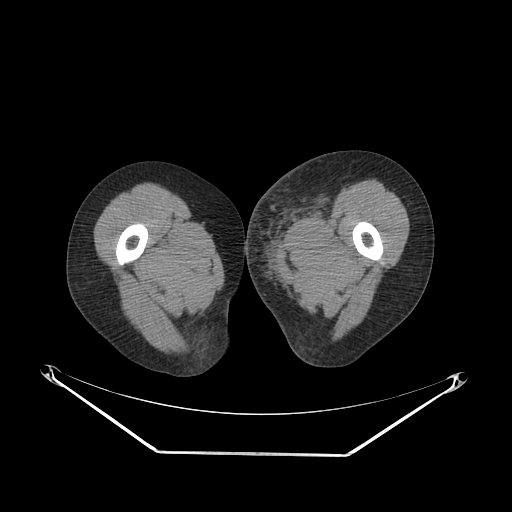
CT of an extremity soft-tissue mass (from a PET/CT study), one axial slice. Position 43 of 267 along the scan axis. 140 kVp. Soft-tissue window (W 400 / L 40 HU). 3.75 mm slice thickness. 512 × 512 image matrix, field of view 500 × 500 mm. Female patient. From the clinical record (not read from this slice): histological type: leiomyosarcoma; grade: high; site of the primary tumour: groin.
Structures marked on this image (expert contour drawn on MRI and transferred to this co-registered scan by the dataset authors):
- gross tumour volume including surrounding oedema: bounding box [x1, y1, x2, y2] px = [244, 180, 330, 255]